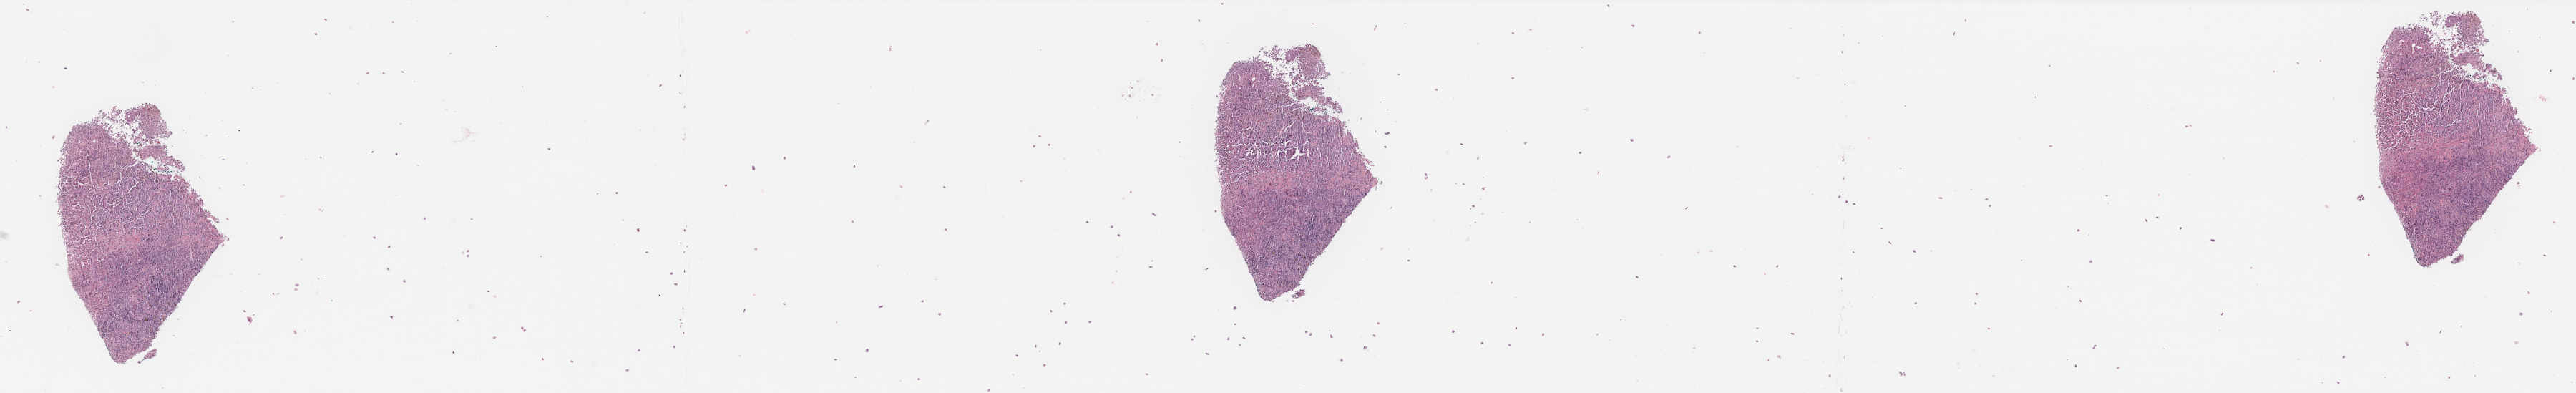
Whole-slide histology image, Hematoxylin and eosin (H&E) stained, low-resolution overview of the scanned area, about 28.9 x 4.4 mm (slide scanned at 40x); formalin-fixed paraffin-embedded (FFPE) diagnostic section; primary tumour sample from the skin. Female patient; age at initial diagnosis 69 years.
Histologic diagnosis: Malignant melanoma, NOS.